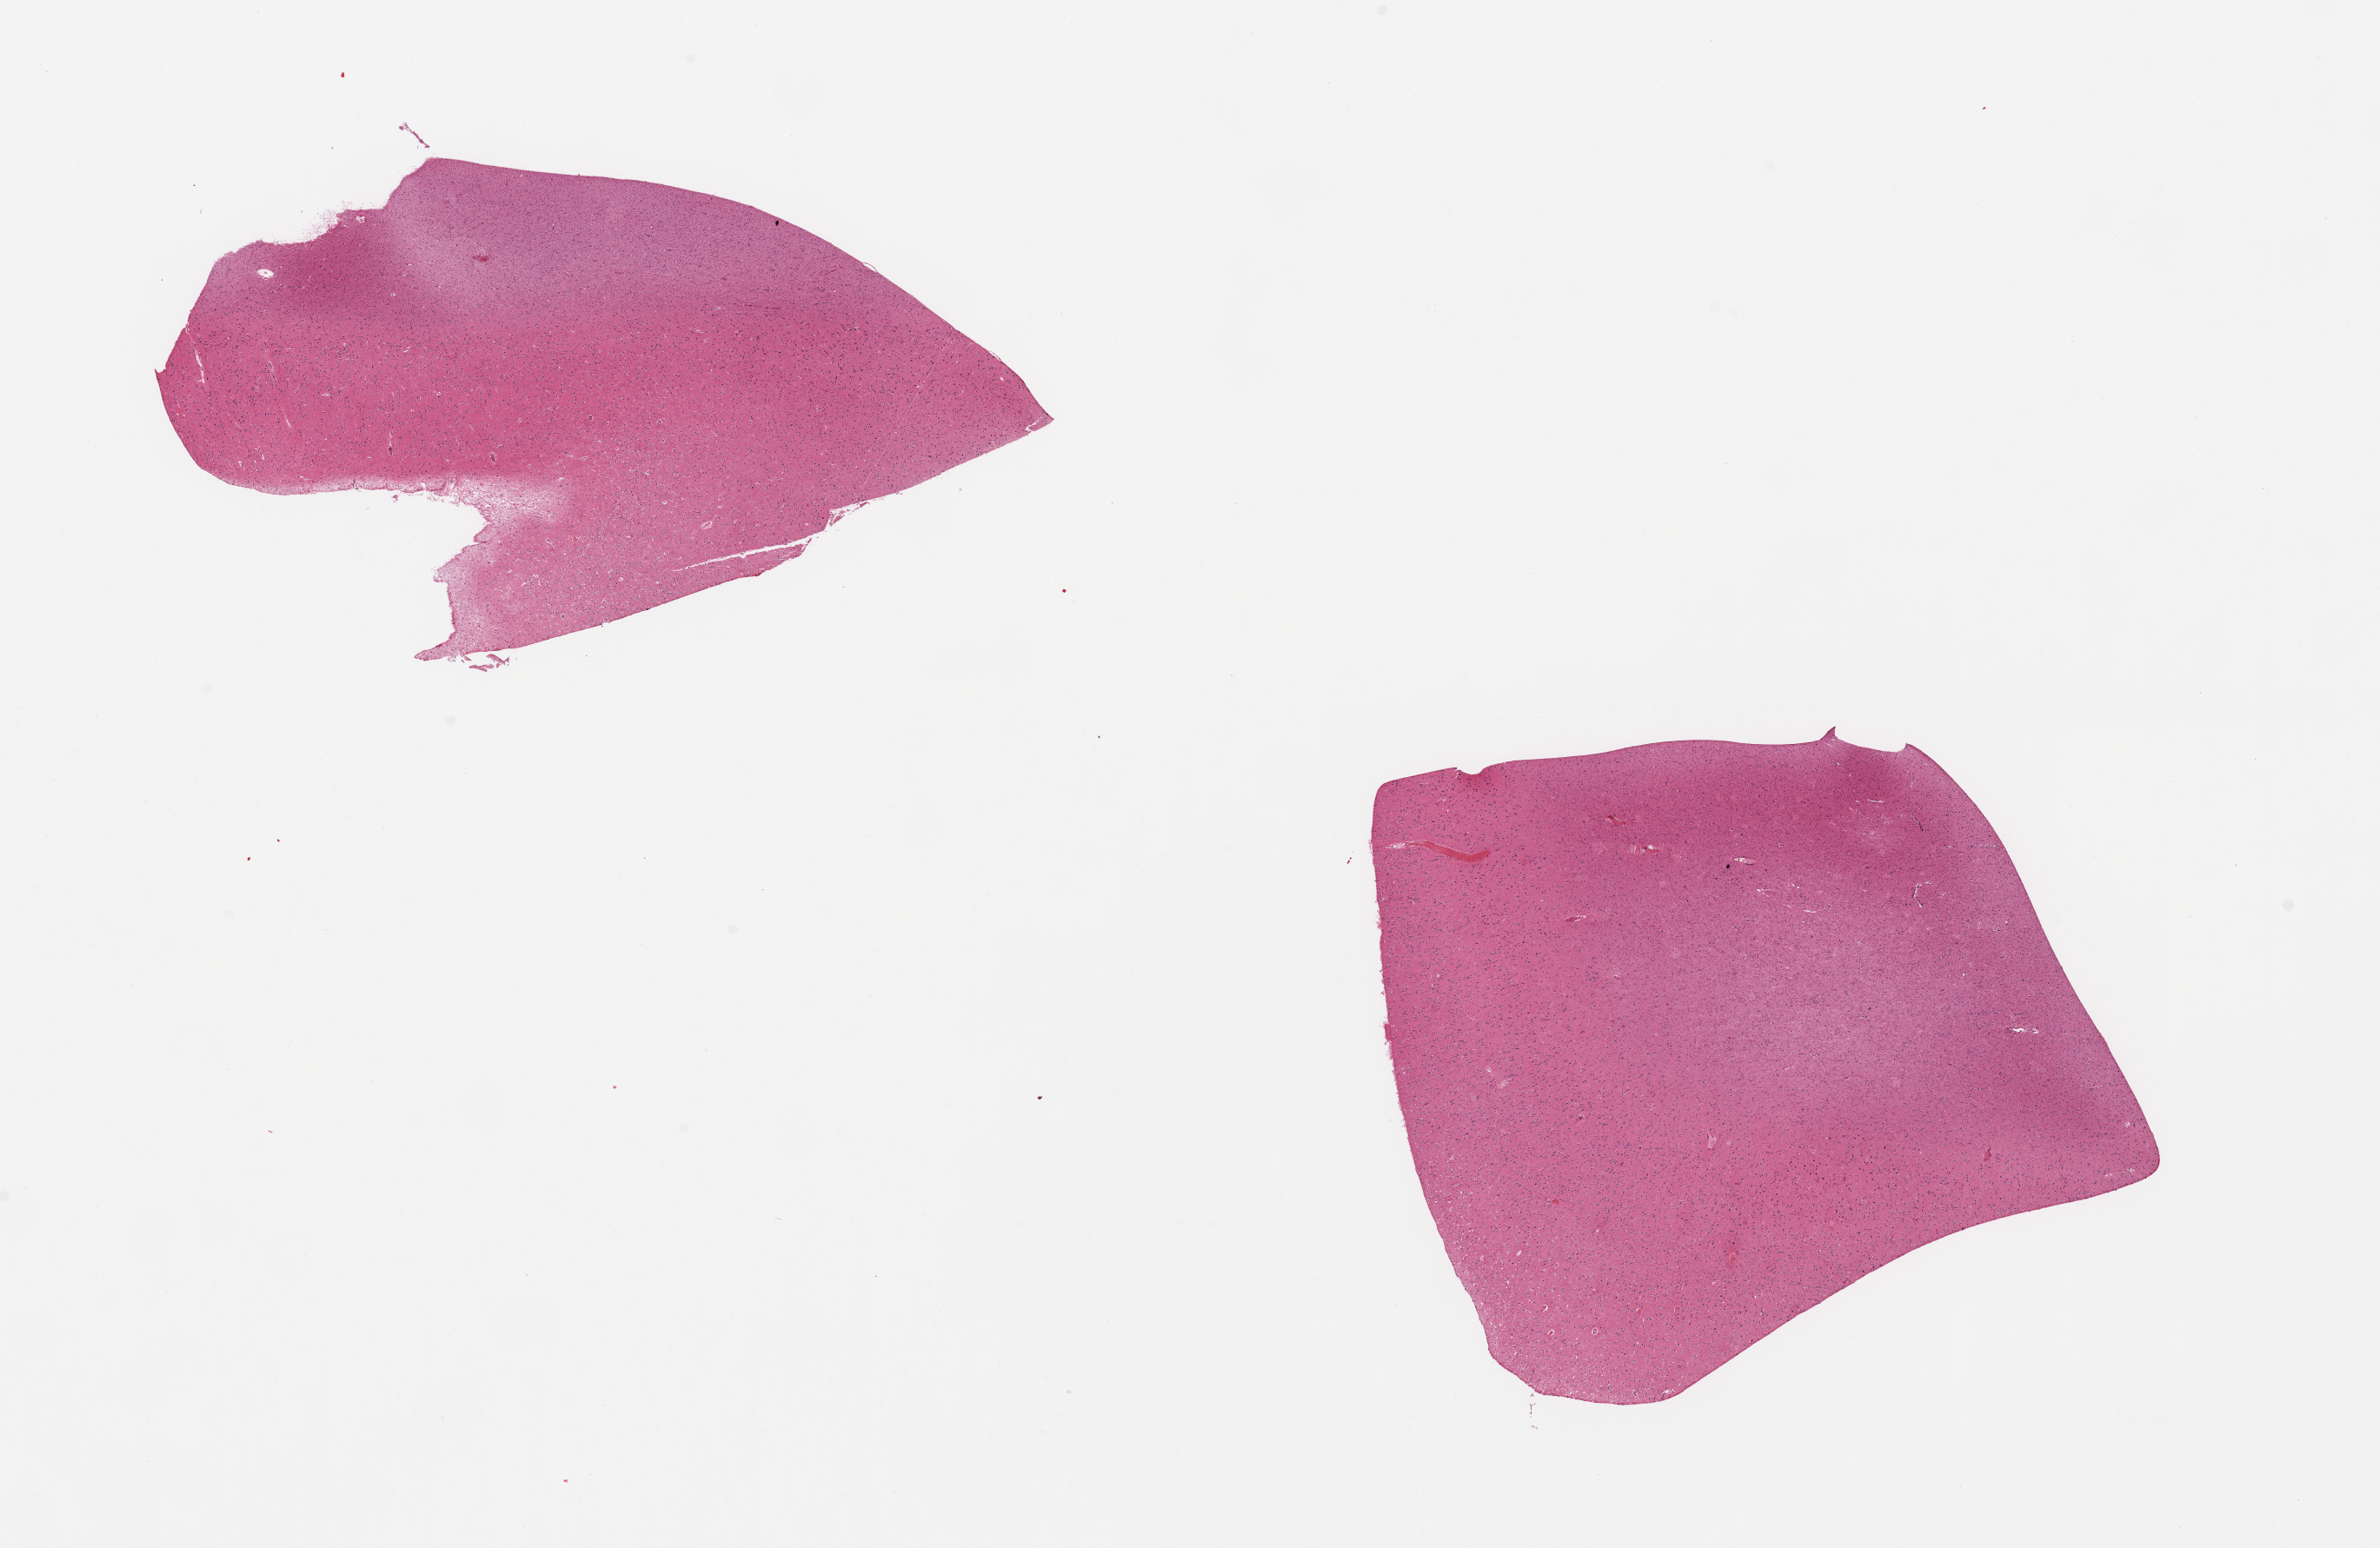
Whole-slide image, H&E stain, shown as a low-resolution overview of the whole scanned area (about 21.7 x 14.1 mm, acquisition: 20x scan). PAXgene-fixed, paraffin-embedded tissue. Sampled site (target tissue): cerebral cortex. Tissue donor sample. Donor: male.
Review note (as recorded): 2 pieces.